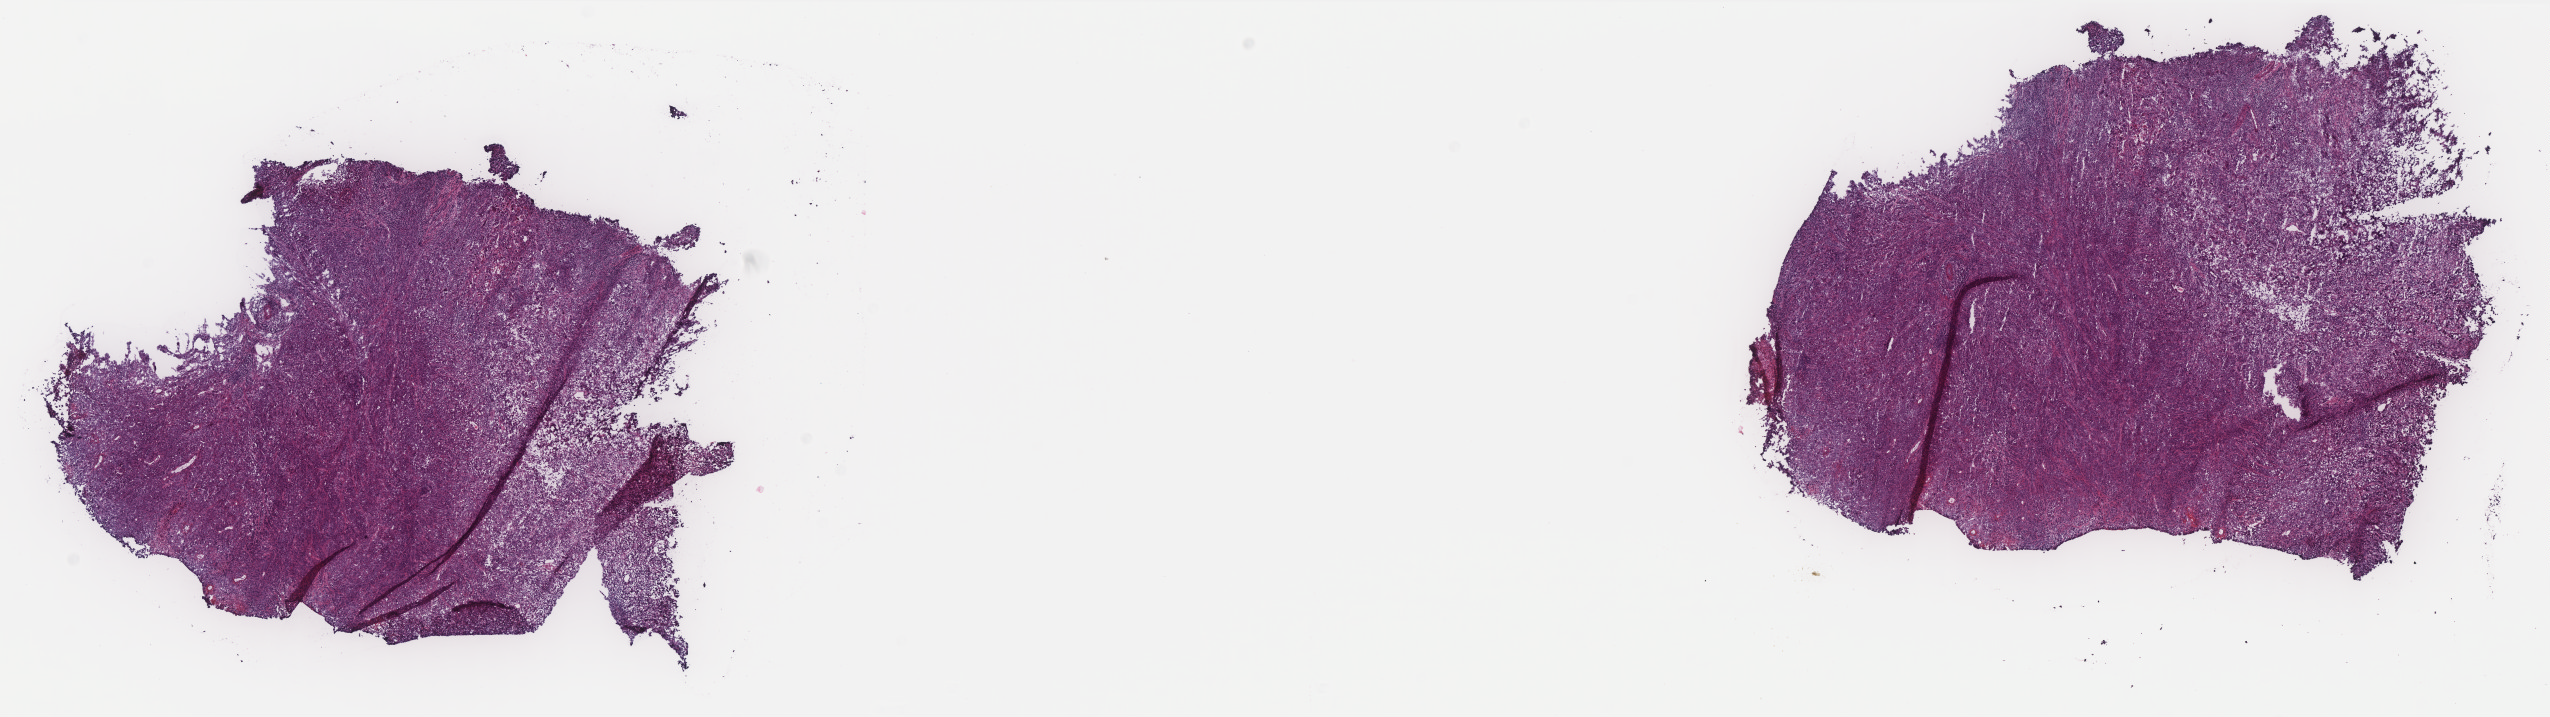
Digitized Hematoxylin and eosin (H&E) stained tissue section (whole slide) — a low-resolution overview of the entire scanned area, about 20.4 x 5.7 mm. Frozen section from the top of the tissue portion. Cervix, primary tumour sample. Patient: female, age at initial diagnosis 35 years. Composition of this section per pathologist review: tumour cells 90%, tumour nuclei 90%.
Pathologic diagnosis: Squamous cell carcinoma, NOS (cervix uteri).